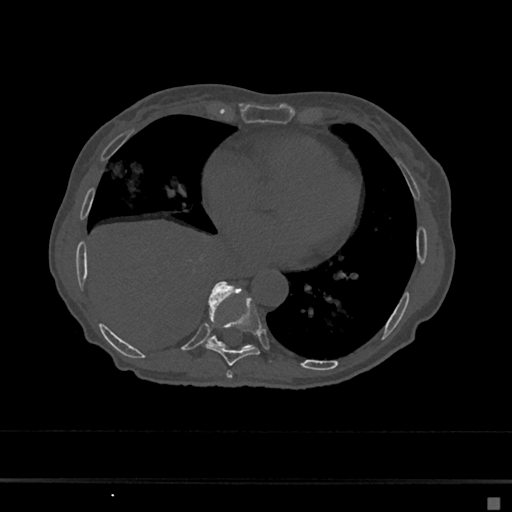
CT including the spine, one axial slice; slice 308 of 797 in the series (ordered by position); reconstruction kernel Br40s/3; 120 kVp; bone window (W 1800 / L 400 HU); 512 × 512 image matrix. Patient: female, 68 years. Case-level facts recorded for this patient, not image findings: primary cancer: renal.
Structures marked on this image (semi-automatic segmentation, software-assisted and operator-edited):
- T7 vertebra: bounding box [x1, y1, x2, y2] px = [226, 371, 233, 379]
- T8 vertebra: [205, 295, 261, 366]
- T9 vertebra: [208, 281, 252, 348]